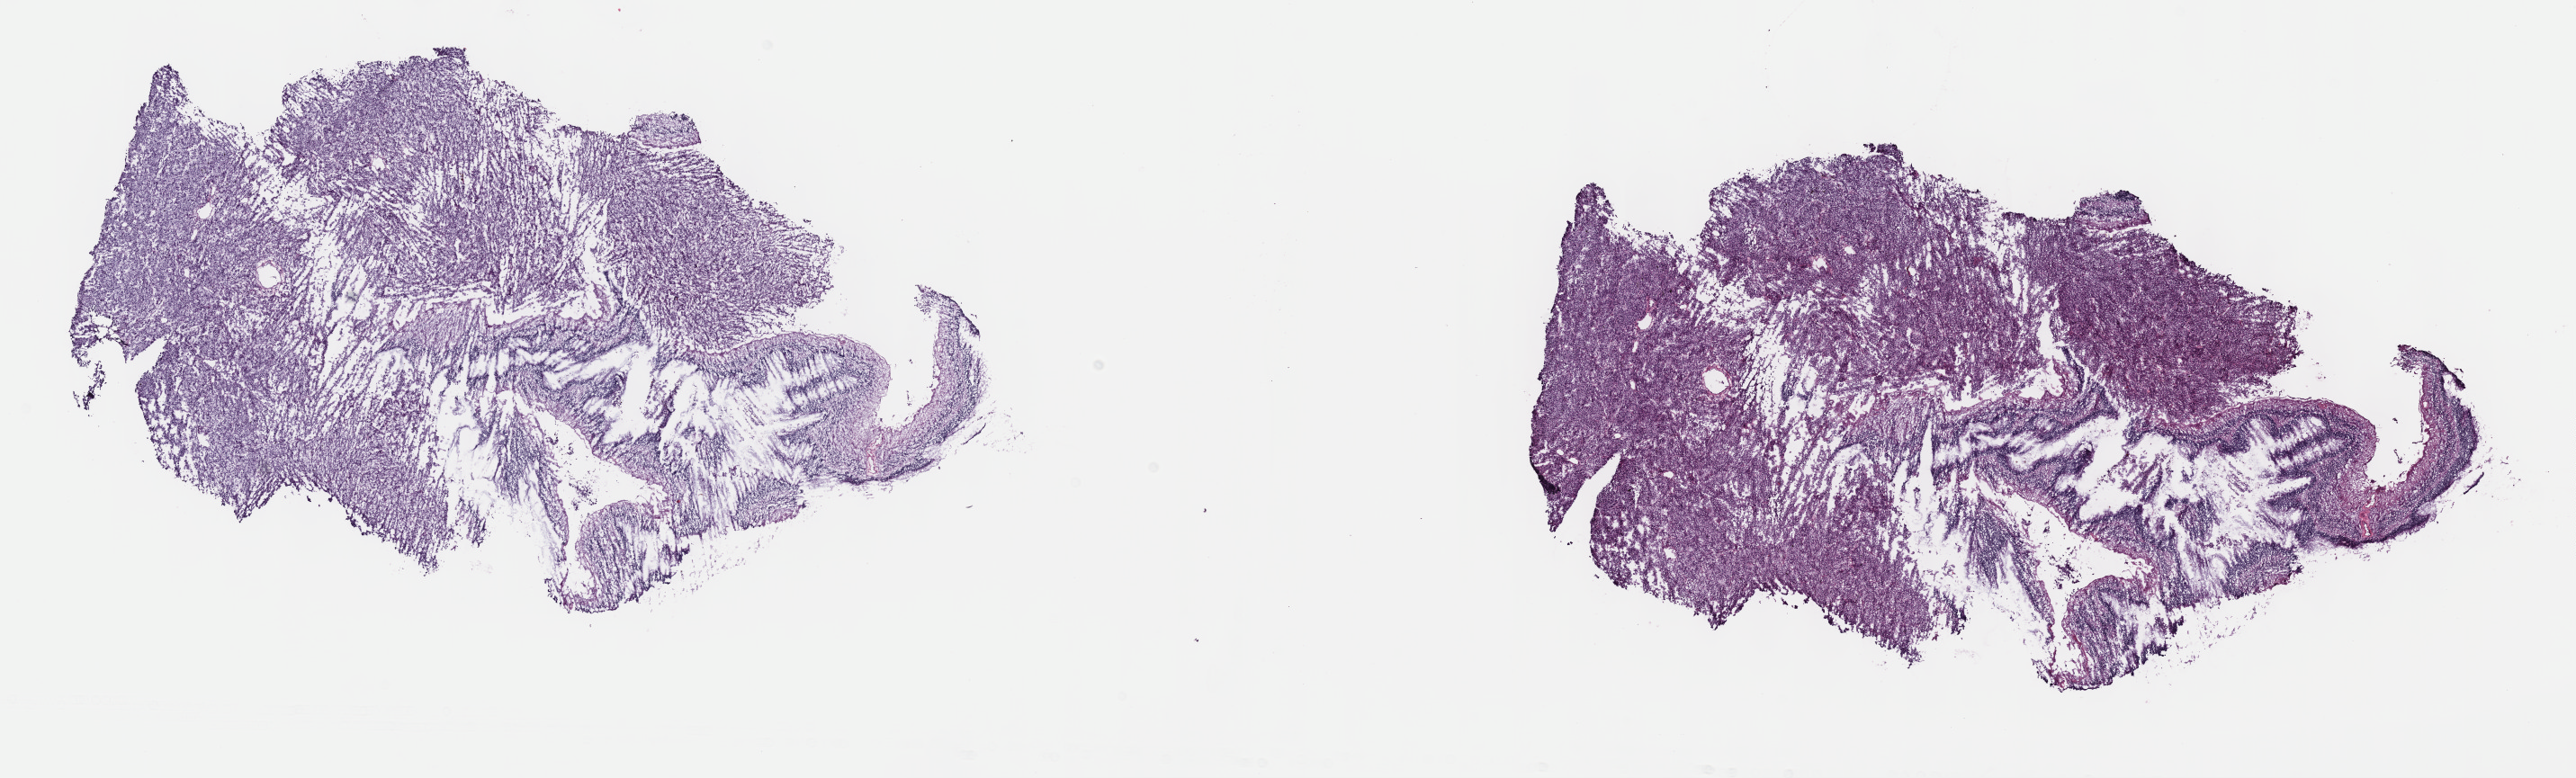
Whole-slide histology image, Hematoxylin and eosin (H&E) stained — a low-resolution overview of the entire scanned area, about 23.2 x 7.0 mm, frozen section, primary tumour sample from the uvea. Male, age 75 years at initial diagnosis. Pathologist review of this section (percent, as recorded): tumour cells 100%, tumour nuclei 80%, normal cells 0%, stromal cells 0%, necrosis 0%. Infiltration values recorded for this section: lymphocyte infiltration 1%, monocyte infiltration 0%, neutrophil infiltration 0%.
AJCC pathologic stage: IIIA (7th edition). TNM: T3b NX MX. Laterality: left. Histologic diagnosis: Mixed epithelioid and spindle cell melanoma (choroid).